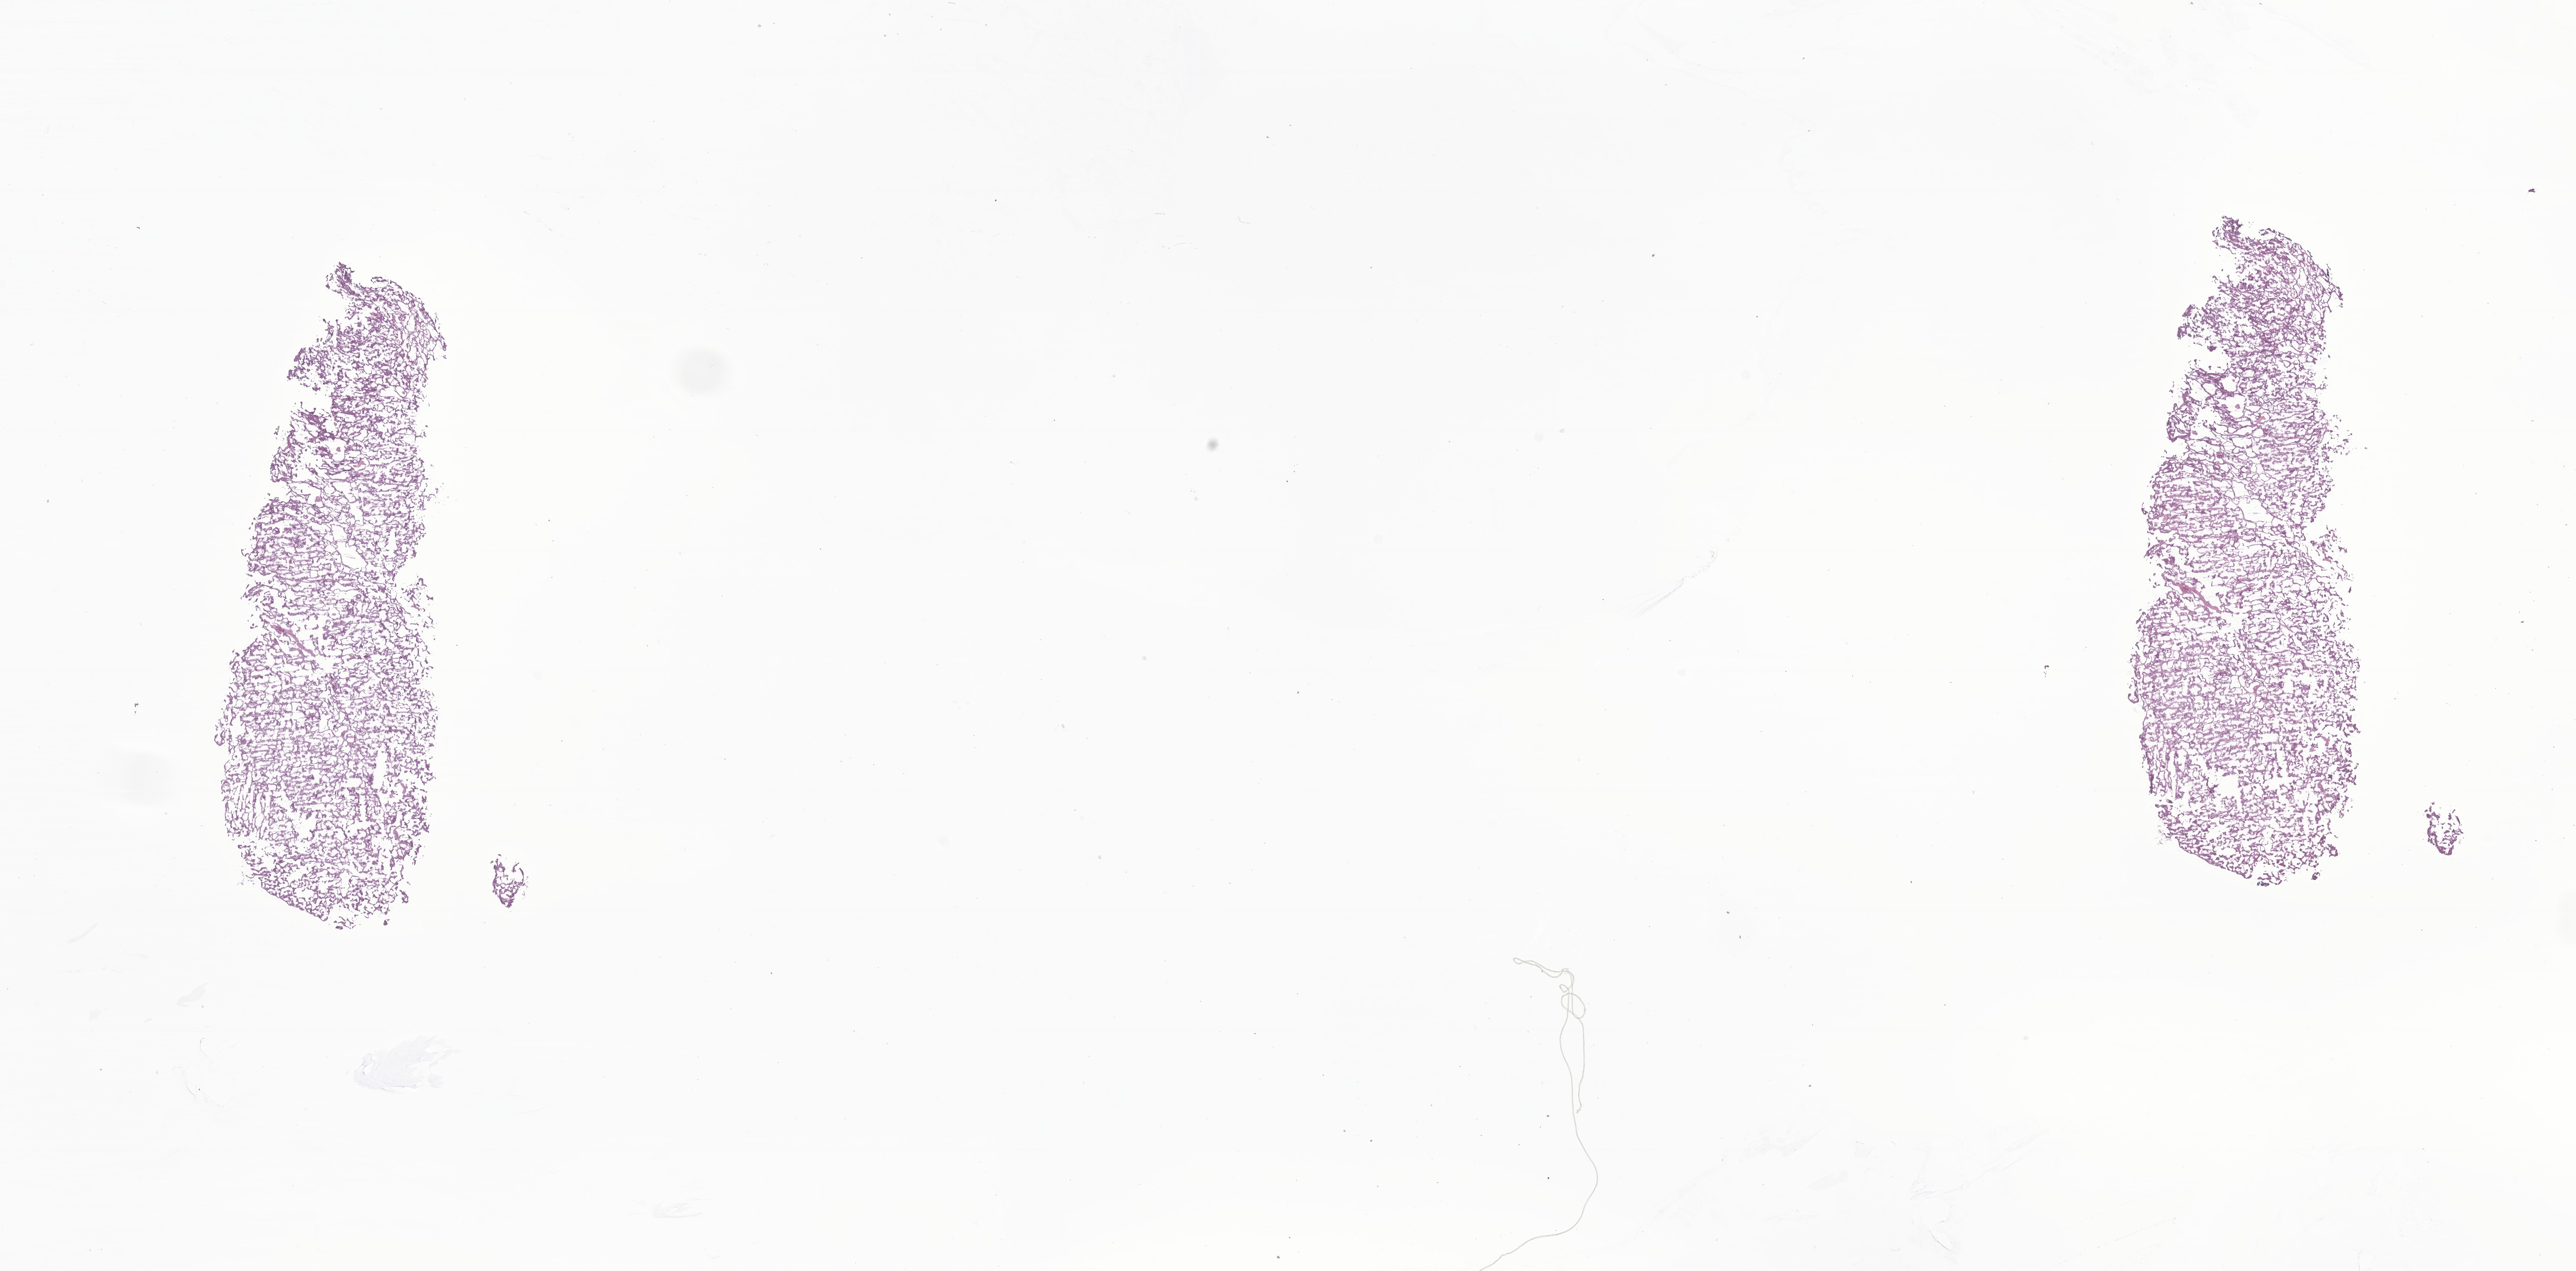
H&E whole-slide image of tumor tissue from the thyroid, shown as a low-resolution overview of the whole scanned area (about 23.0 x 11.3 mm), cryosection (OCT / tissue freezing medium). Patient: female, age 218 months (18 years 2 months).
Diagnosis (ICD-O-3 morphology term): Papillary carcinoma, NOS.